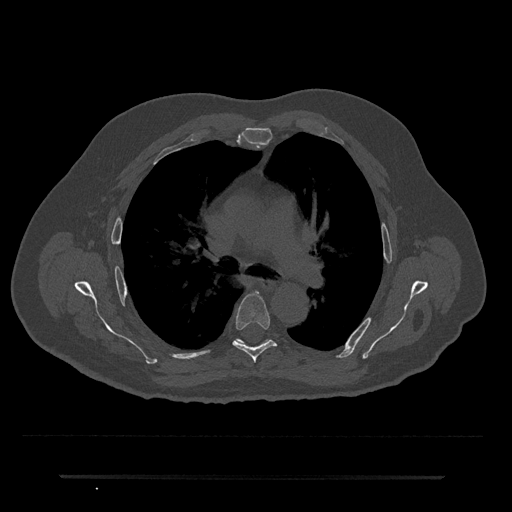
CT including the spine, one axial slice; position 477 of 797 along the scan axis; reconstruction kernel Br40s/3; 120 kVp; bone window (W 1800 / L 400 HU); 0.5 mm slice thickness; 512 × 512 image matrix. Male patient, age 69 years. From the clinical record (not read from this slice): primary cancer: prostate.
Structures marked on this image (semi-automatically segmented with operator editing):
- T5 vertebra: bounding box [x1, y1, x2, y2] px = [233, 291, 277, 362]